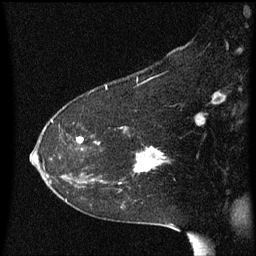
Breast MRI (dynamic contrast-enhanced), one sagittal slice. Slice 38 of 60 in the series (ordered by position). Dynamic contrast-enhanced series, image 2 of 3 at this slice position (ordered by acquisition). 1.5 T. TE 4.2 ms, TR 8.4 ms. 2 mm slice thickness. 256 × 256 image matrix, field of view 200 × 200 mm. Patient: female, 54 years. Case-level facts recorded for this patient, not image findings: setting: breast cancer imaged before/during neoadjuvant chemotherapy; receptor status: HR-positive, HER2-negative.
Structures marked on this image (semi-automatic segmentation, software-assisted and operator-edited):
- analysis volume of interest (the breast-tissue region the enhancement analysis was run in; not a lesion): box from (x=117, y=132) to (x=171, y=185) px
- tumour enhancement mask (voxels above the 70 % enhancement threshold inside the analysis volume of interest): (x=136, y=148)–(x=166, y=173)